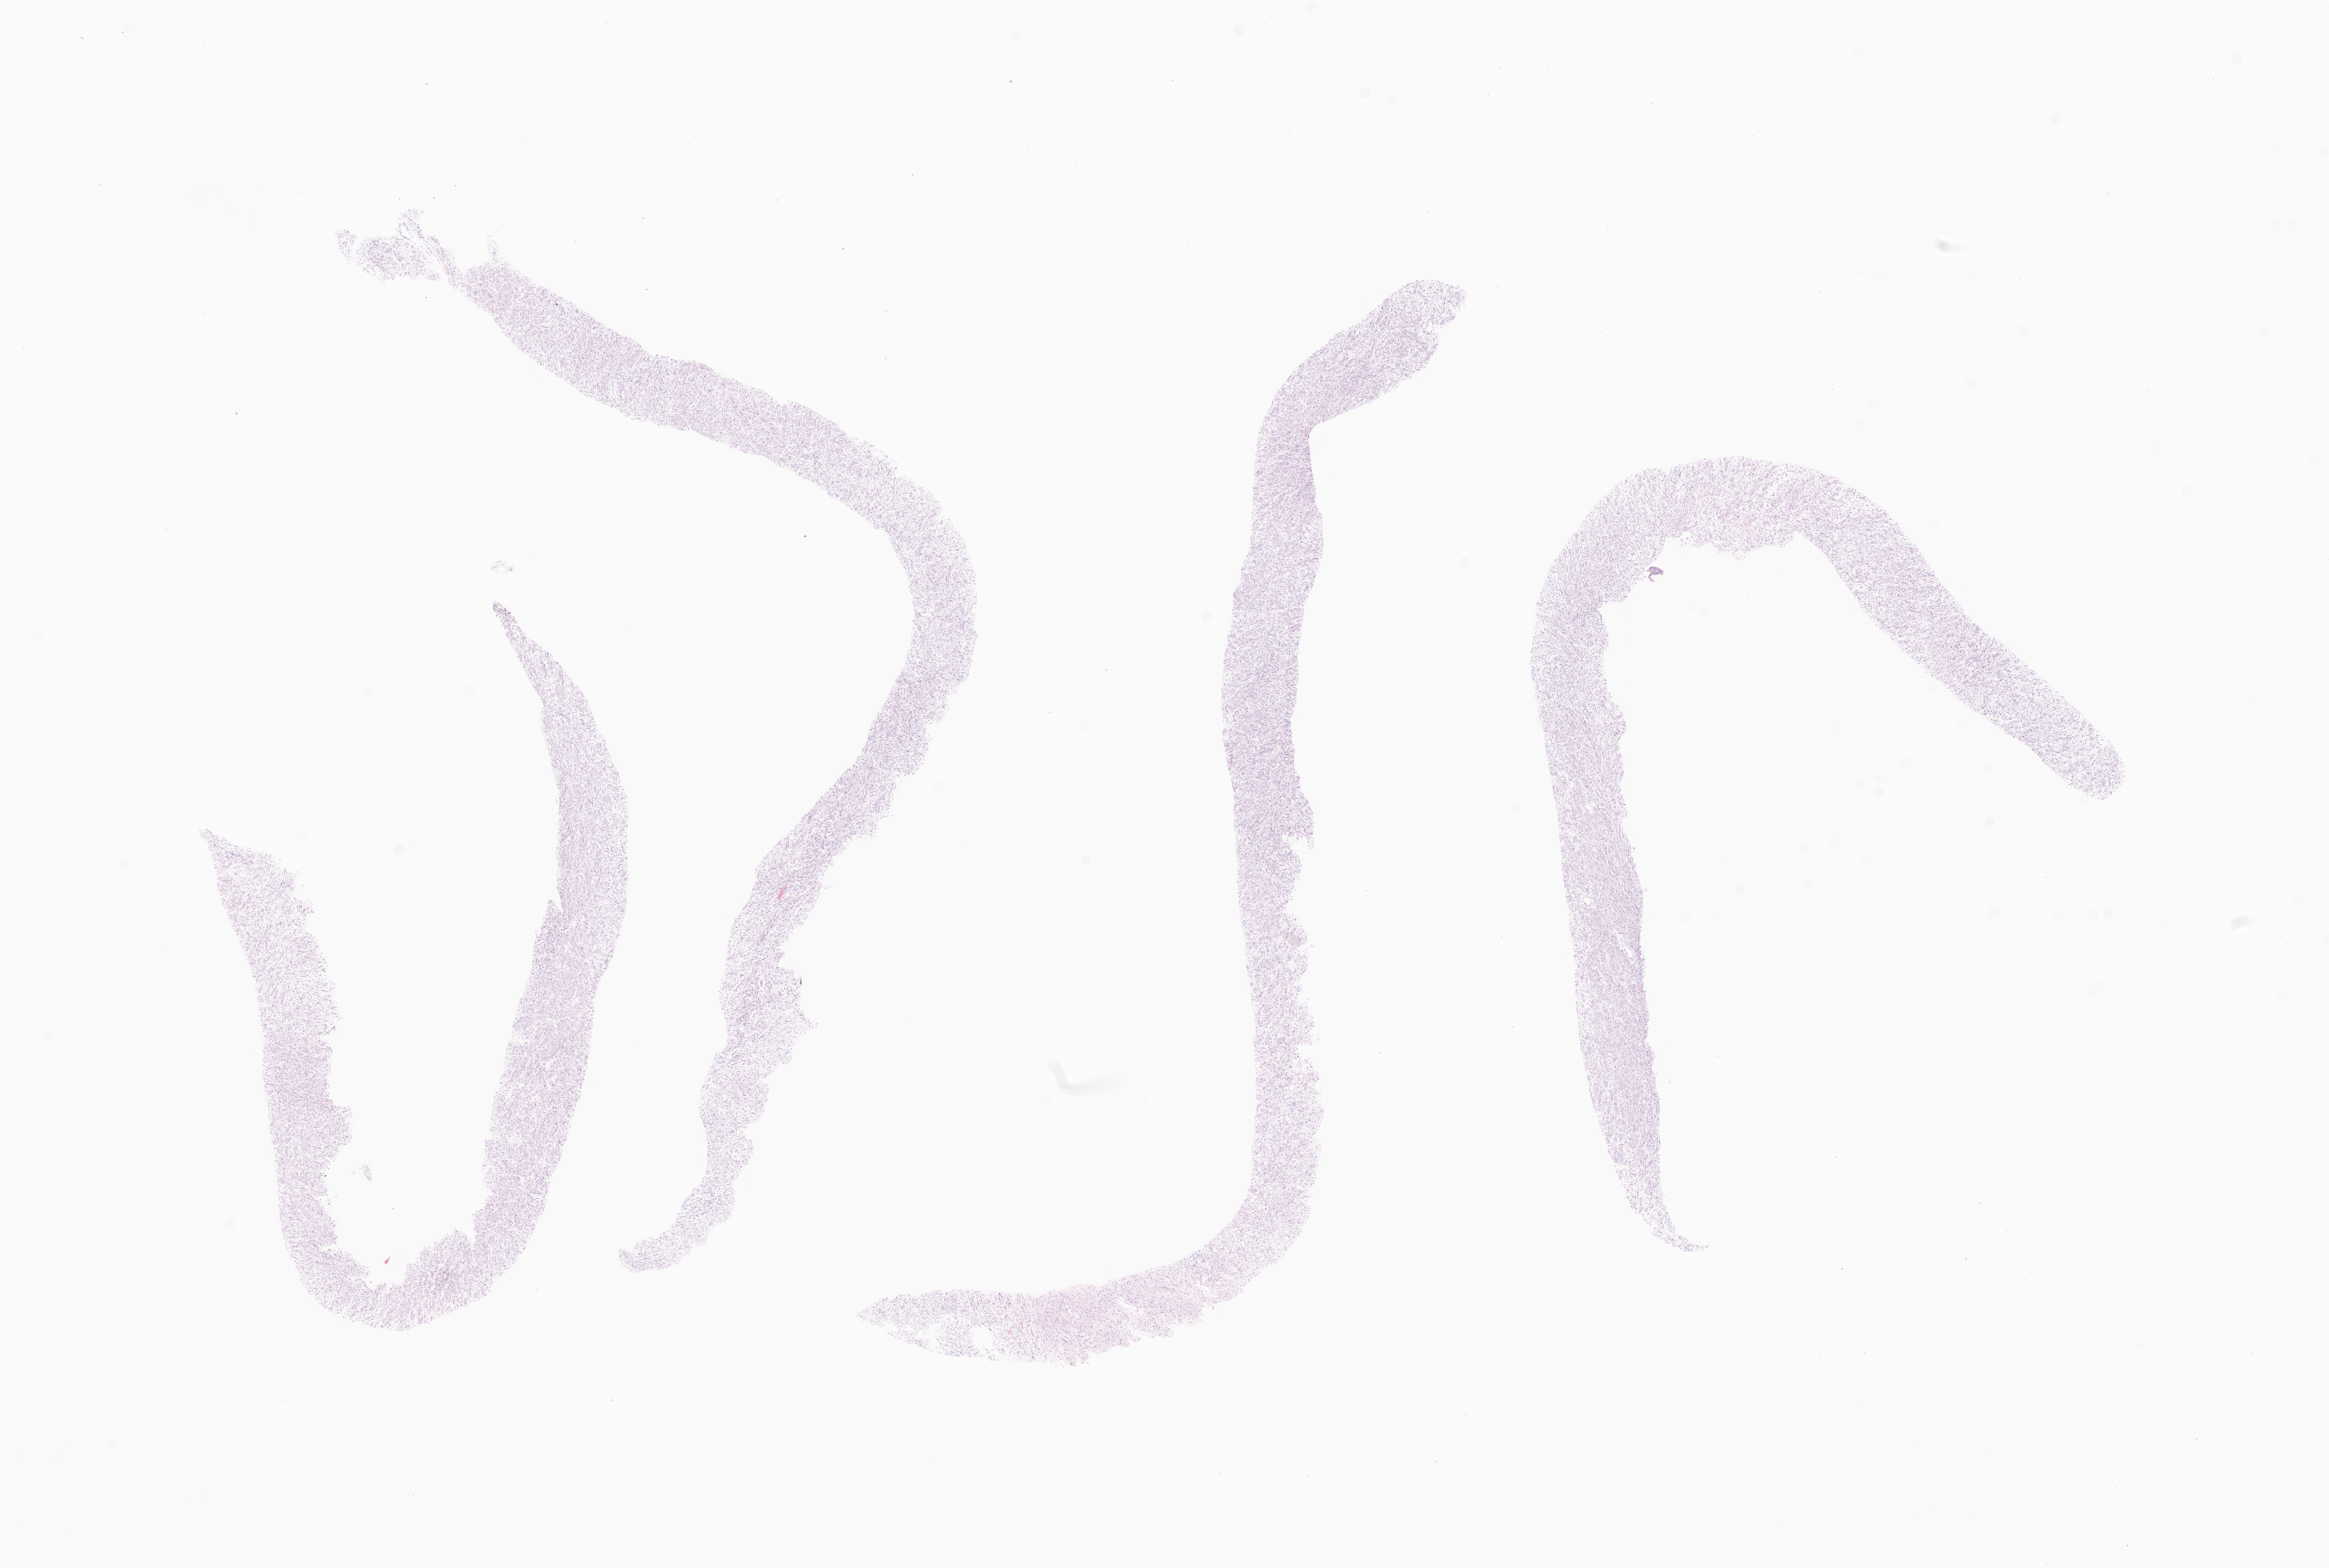
Whole-slide image, haematoxylin and eosin stain of tumor tissue from the soft tissue of lower extremity, whole scanned area (about 21.0 x 14.1 mm) shown as a low-resolution overview, formalin-fixed, paraffin-embedded (FFPE) tissue. Patient female; age 137 days.
Diagnosis: Rhabdomyosarcoma, NOS. Tissue or organ of origin (case record): connective, subcutaneous and other soft tissues of lower limb and hip.